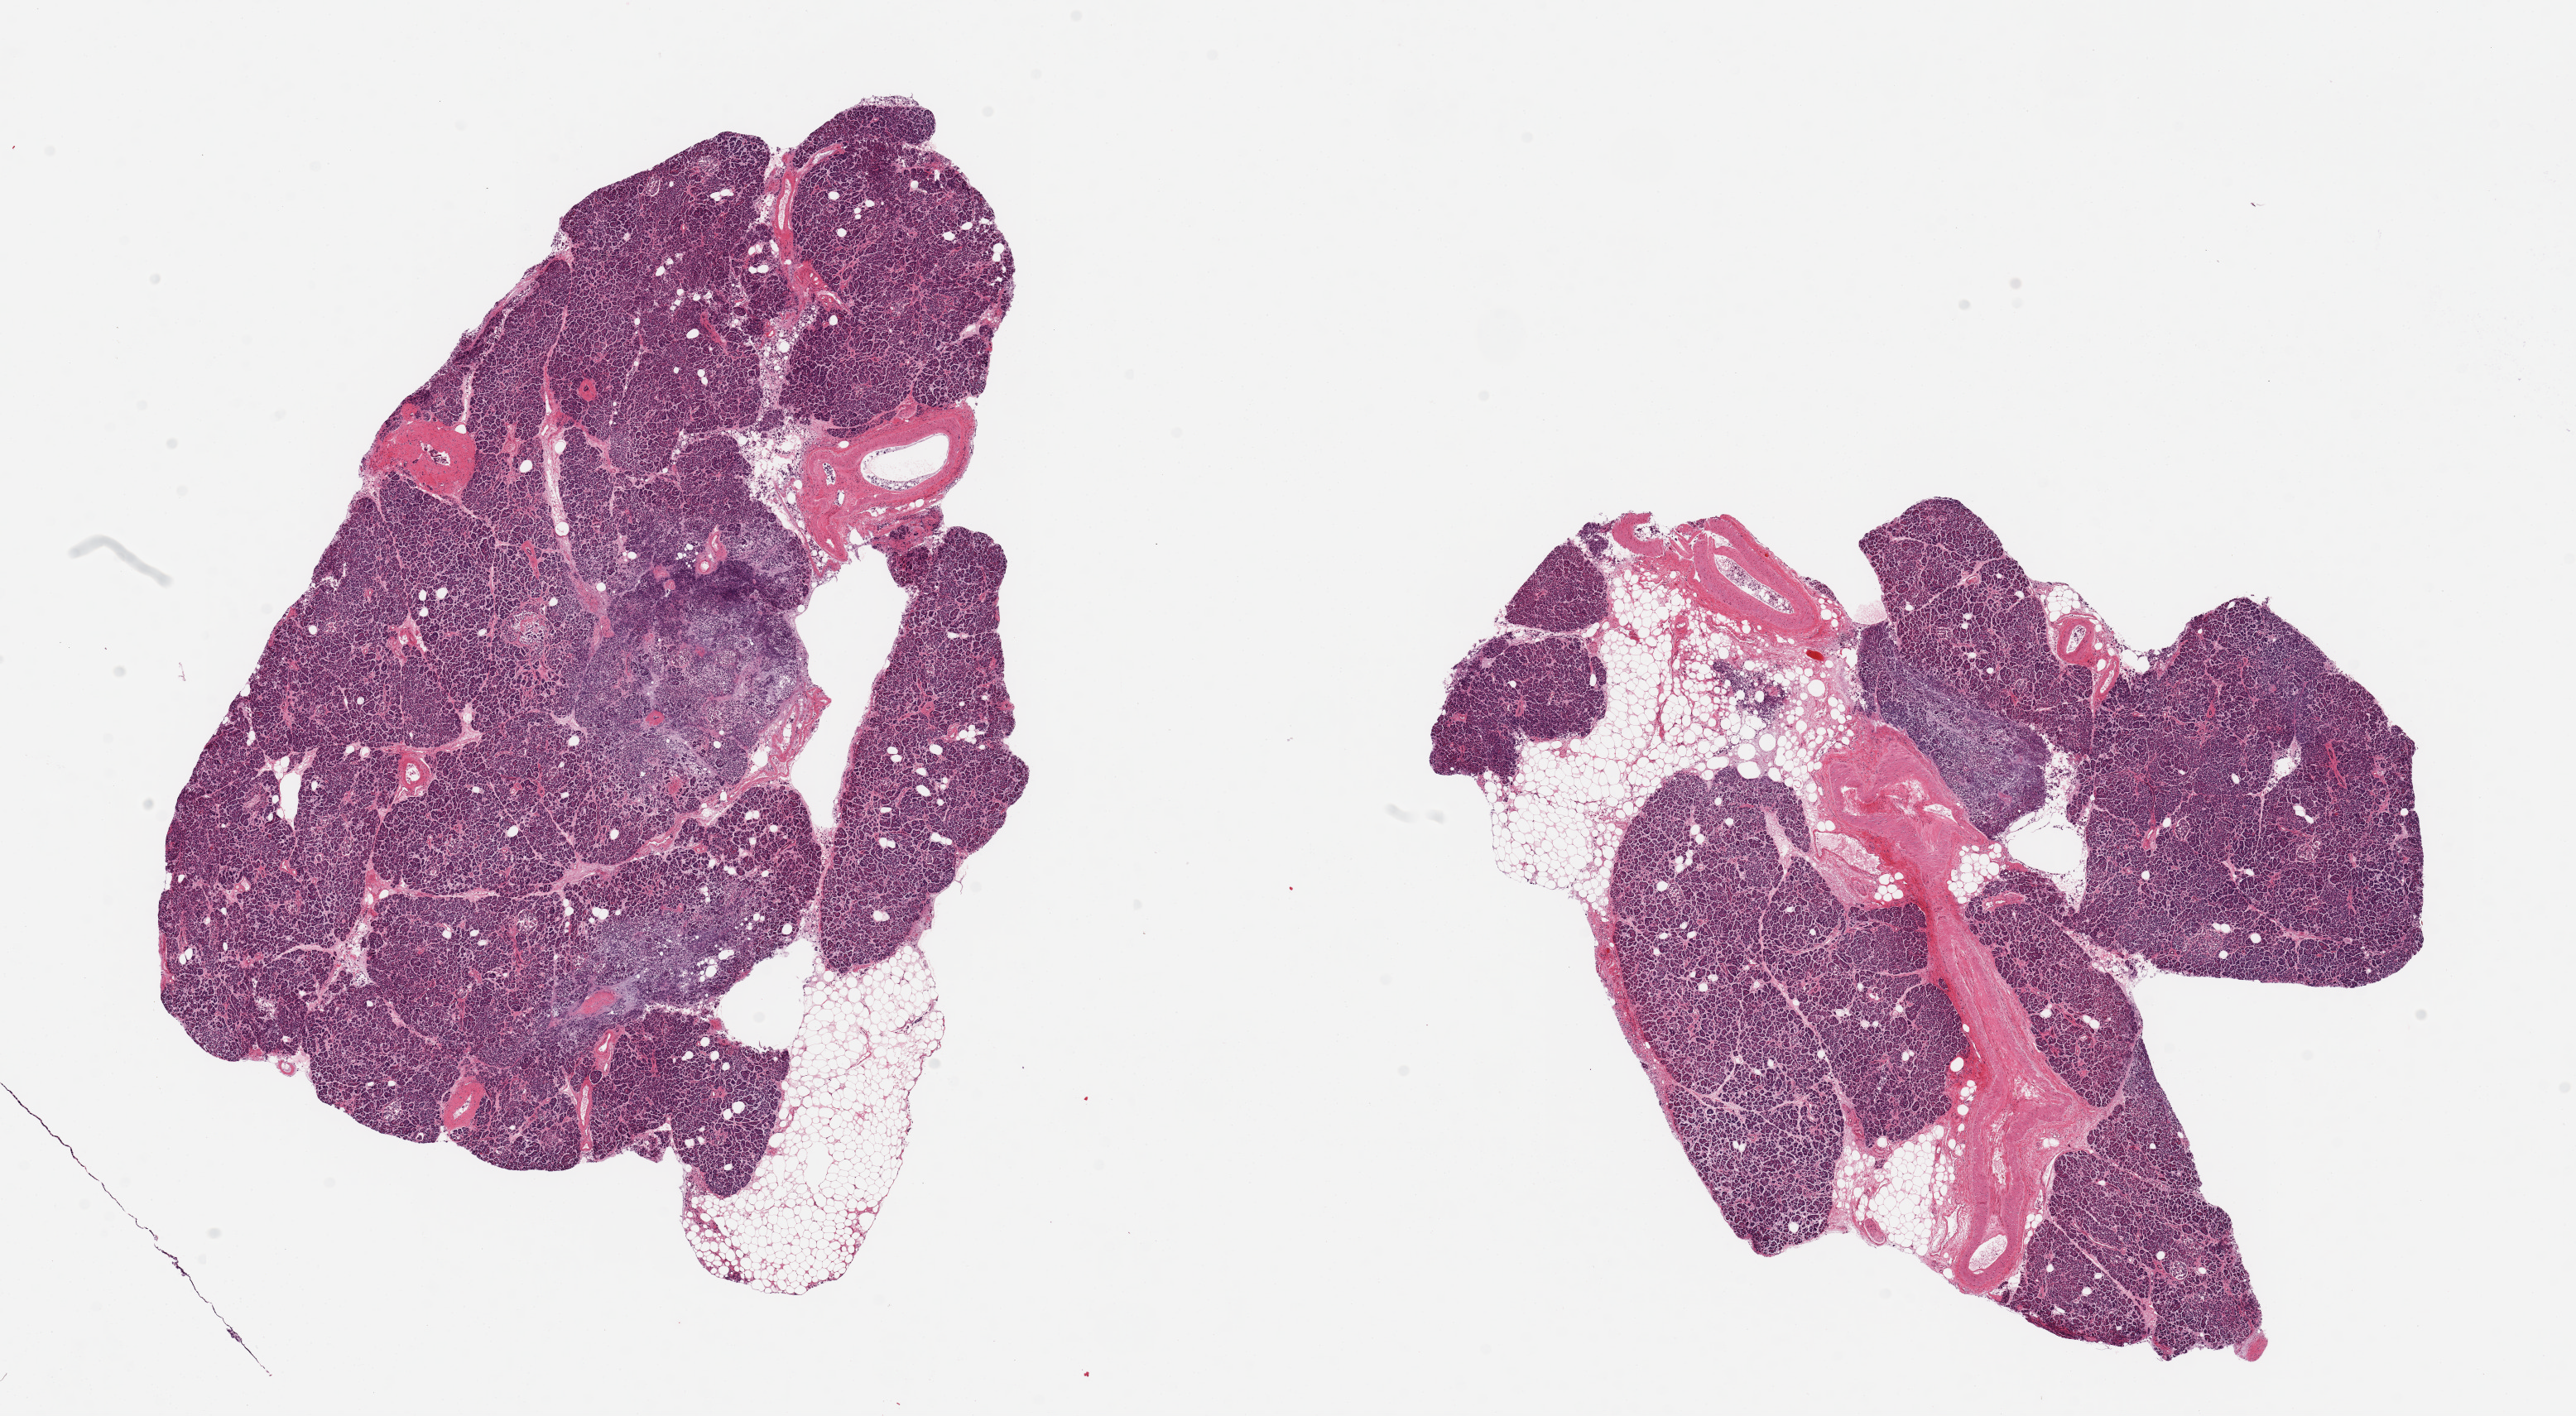
Hematoxylin and eosin (H&E) whole-slide image, brightfield, low-resolution overview of the scanned area, about 24.6 x 13.5 mm (slide scanned at 20x). PAXgene-fixed, paraffin-embedded tissue. Section of pancreas (target tissue). Tissue donor sample. Female donor.
Review note (as recorded): 2 pieces, includes 10-20% fat, moderate to severe autolysis, intraacinar and perilobular fibrosis.